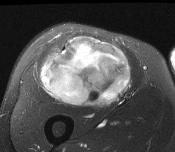
MRI of an extremity soft-tissue mass, one axial slice; position 90 of 116 along the scan axis; T2-weighted fat-saturated; MR volume resampled by the dataset authors to the PET/CT grid (not the native acquisition matrix); 3.27 mm slice thickness; 175 × 152 image matrix. Male patient. From the clinical record (not read from this slice): histological type: pleiomorphic leiomyosarcoma; grade: intermediate; site of the primary tumour: right thigh.
Annotated regions visible in this slice (expert contour drawn on MRI and transferred to this co-registered scan by the dataset authors):
- gross tumour volume including surrounding oedema: bounding box (x1, y1, x2, y2) in pixels: (40, 38, 132, 107)
- gross tumour volume (mass): (40, 38, 132, 107)